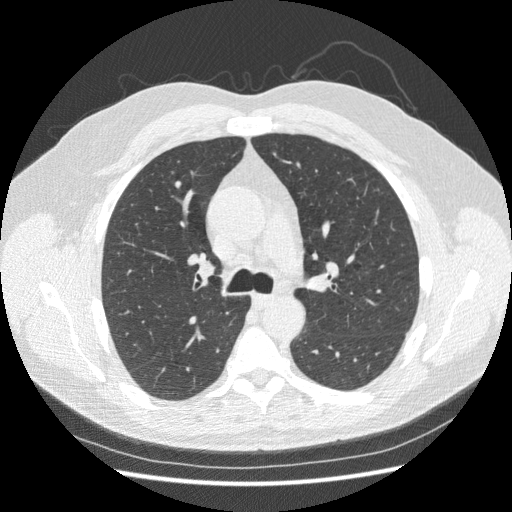
Low-dose screening chest CT, axial slice. Baseline screening round. Lung window (W 1500 / L -600 HU). 1.25 mm slice thickness. 512 × 512 image matrix, field of view 360 × 360 mm. Male, age 63 years at enrolment.
Expert reader's lesion annotation, bounding box <167,175,188,191> (left, top, right, bottom; pixels). Screening reader's record for this exam (one nodule recorded; not confirmed to be the boxed lesion): non-calcified nodule or mass ≥4 mm, right upper lobe, 5 × 4 mm, smooth margins, soft tissue attenuation. Official screen result: positive, change unspecified: nodule(s) >= 4 mm or enlarging nodule(s), mass(es), or other non-specific abnormalities suspicious for lung cancer.